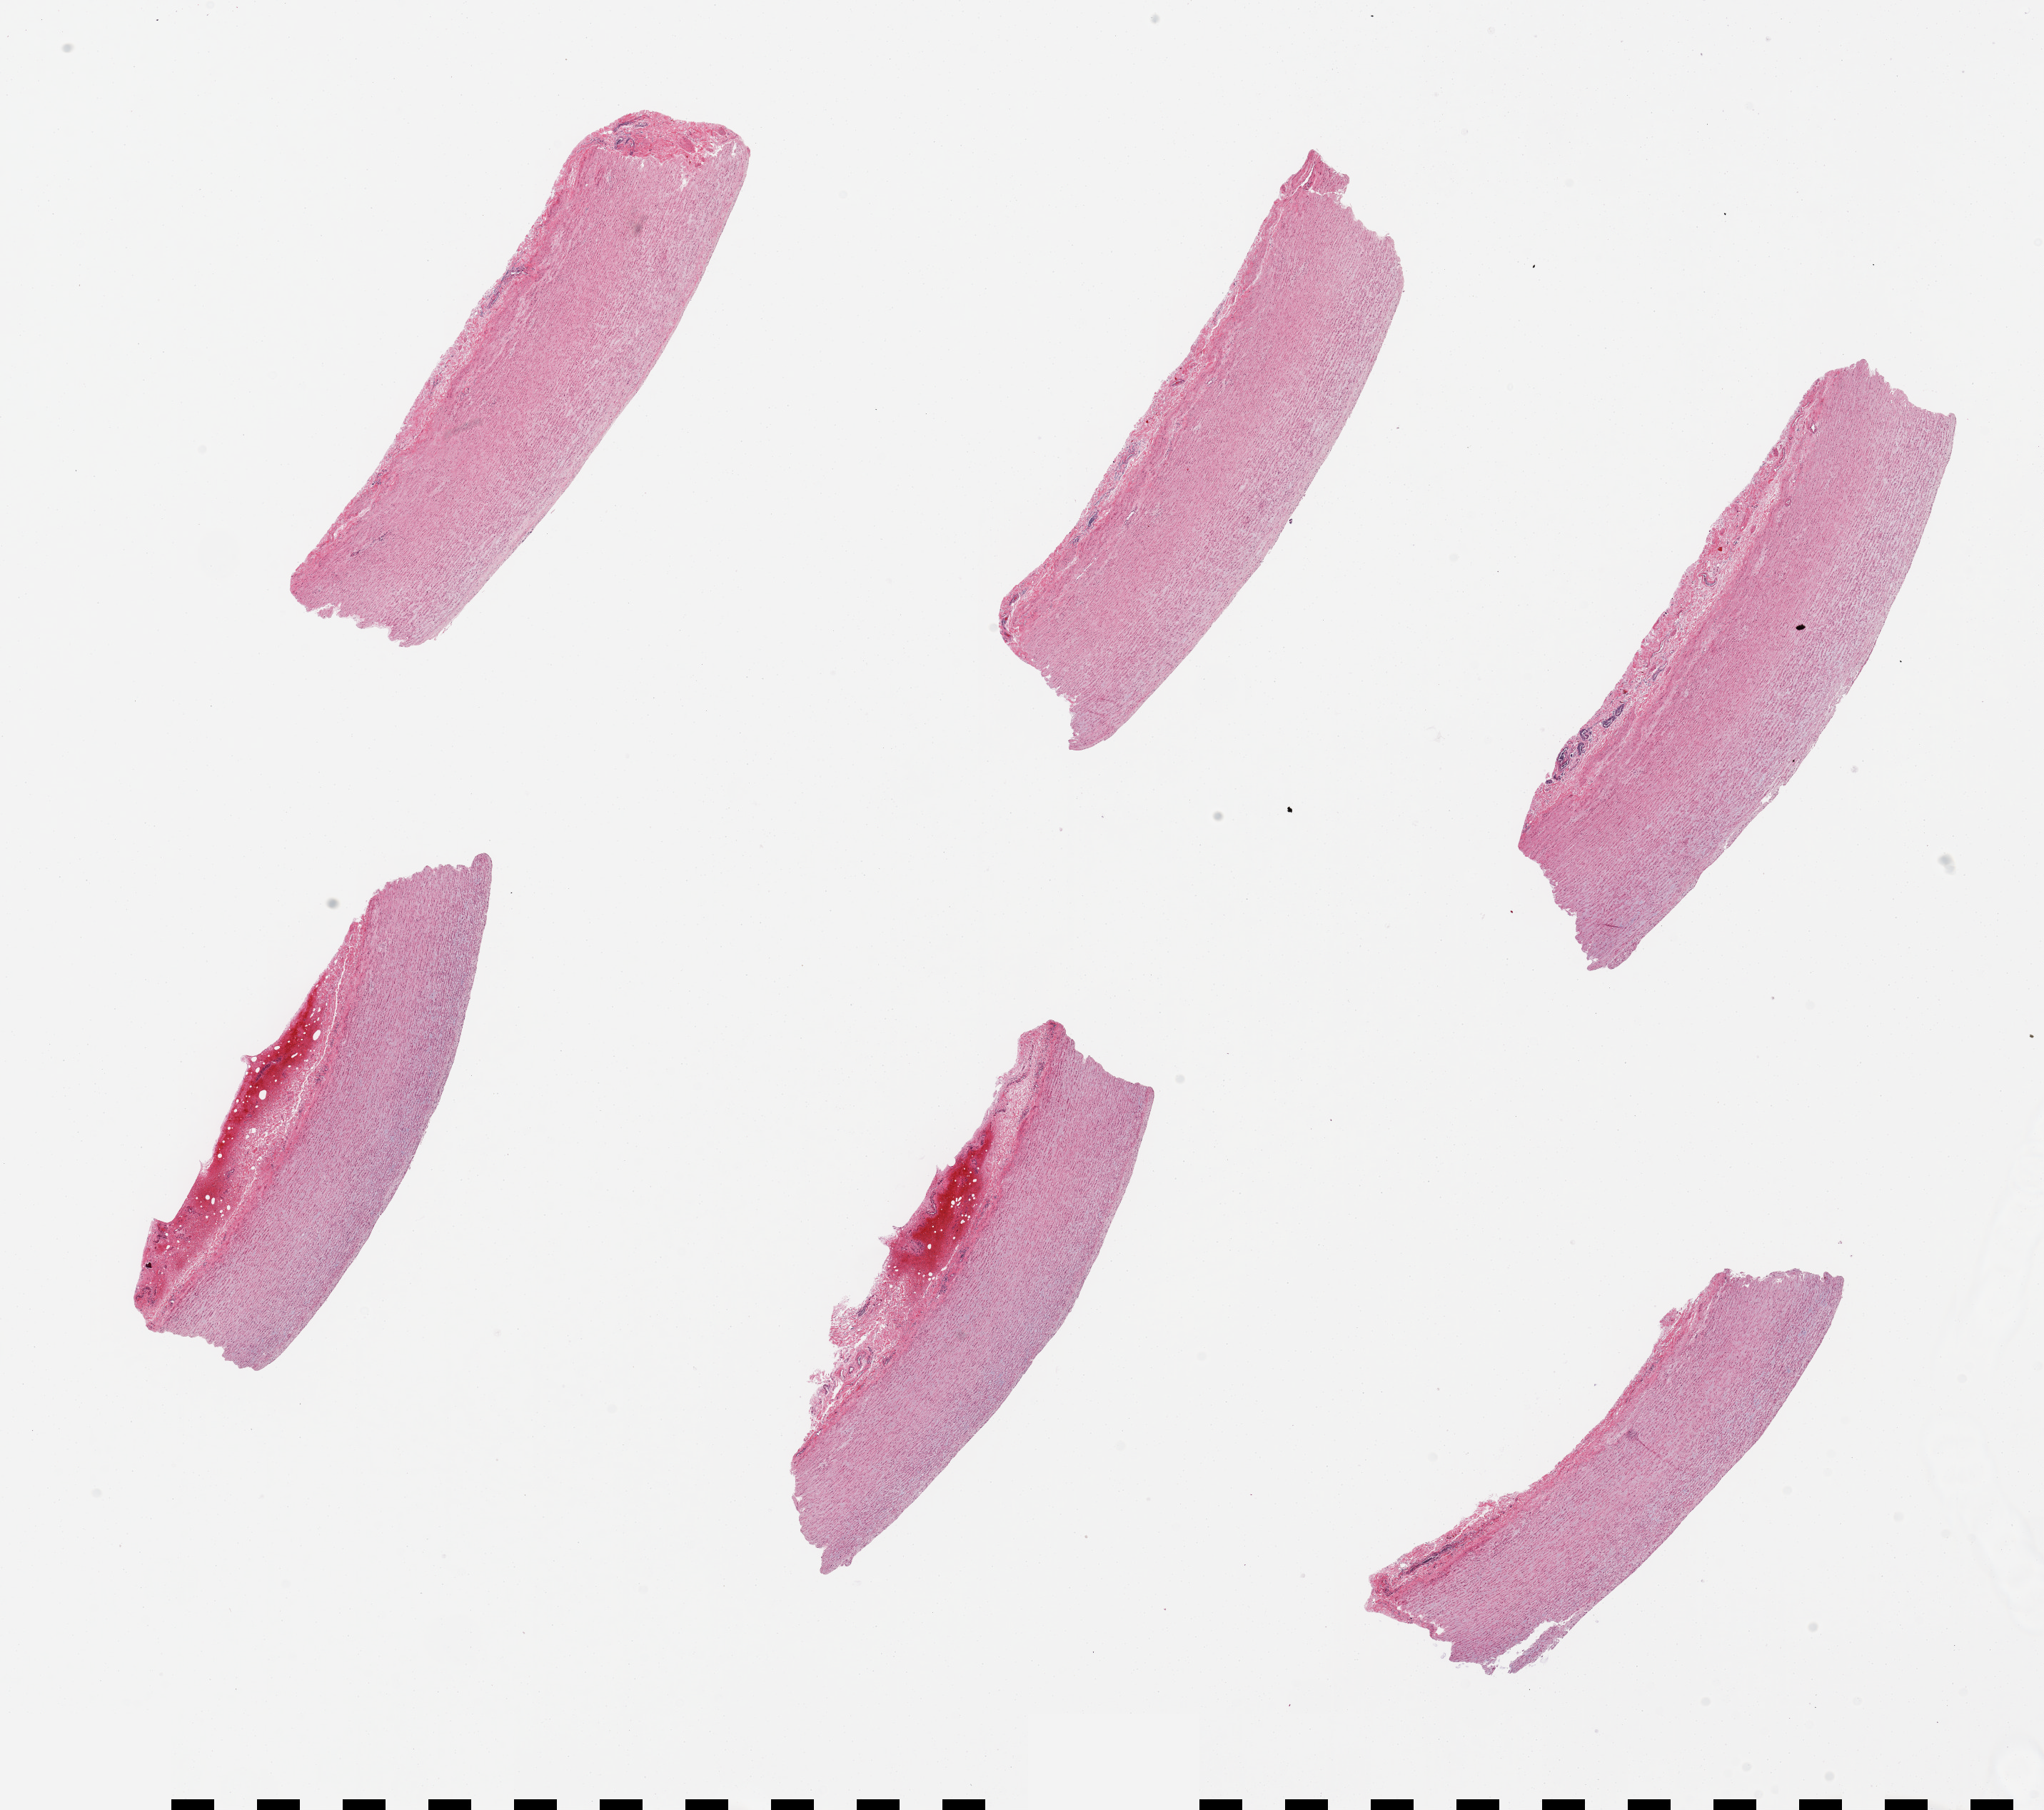
Whole-slide image, hematoxylin and eosin (H&E) stain — a low-resolution overview of the entire scanned area, about 22.6 x 20.0 mm. PAXgene-fixed, paraffin-embedded tissue. Sampled site (target tissue): aorta. Tissue donor sample.
Reviewer comment on this tissue sample: 6pieces, up to 7x2mm.